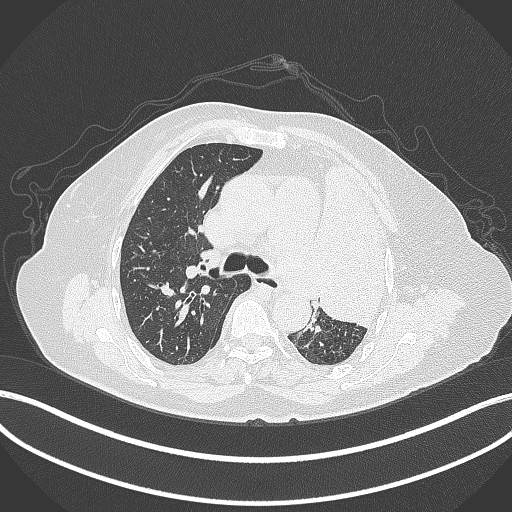
Chest CT, one axial slice; slice 253 of 399 in the series (ordered by position); lung window (W 1500 / L -600 HU); 512 × 512 image matrix, field of view 400 × 400 mm. Female patient, age 75 years. Case-level facts recorded for this patient, not image findings: clinical TNM (as recorded): T3 N3 M1.
Structures marked on this image (rectangle marked by the reading radiologist):
- lung tumour (recorded histology: adenocarcinoma): bounding box <312,157,391,331> (left, top, right, bottom; pixels)